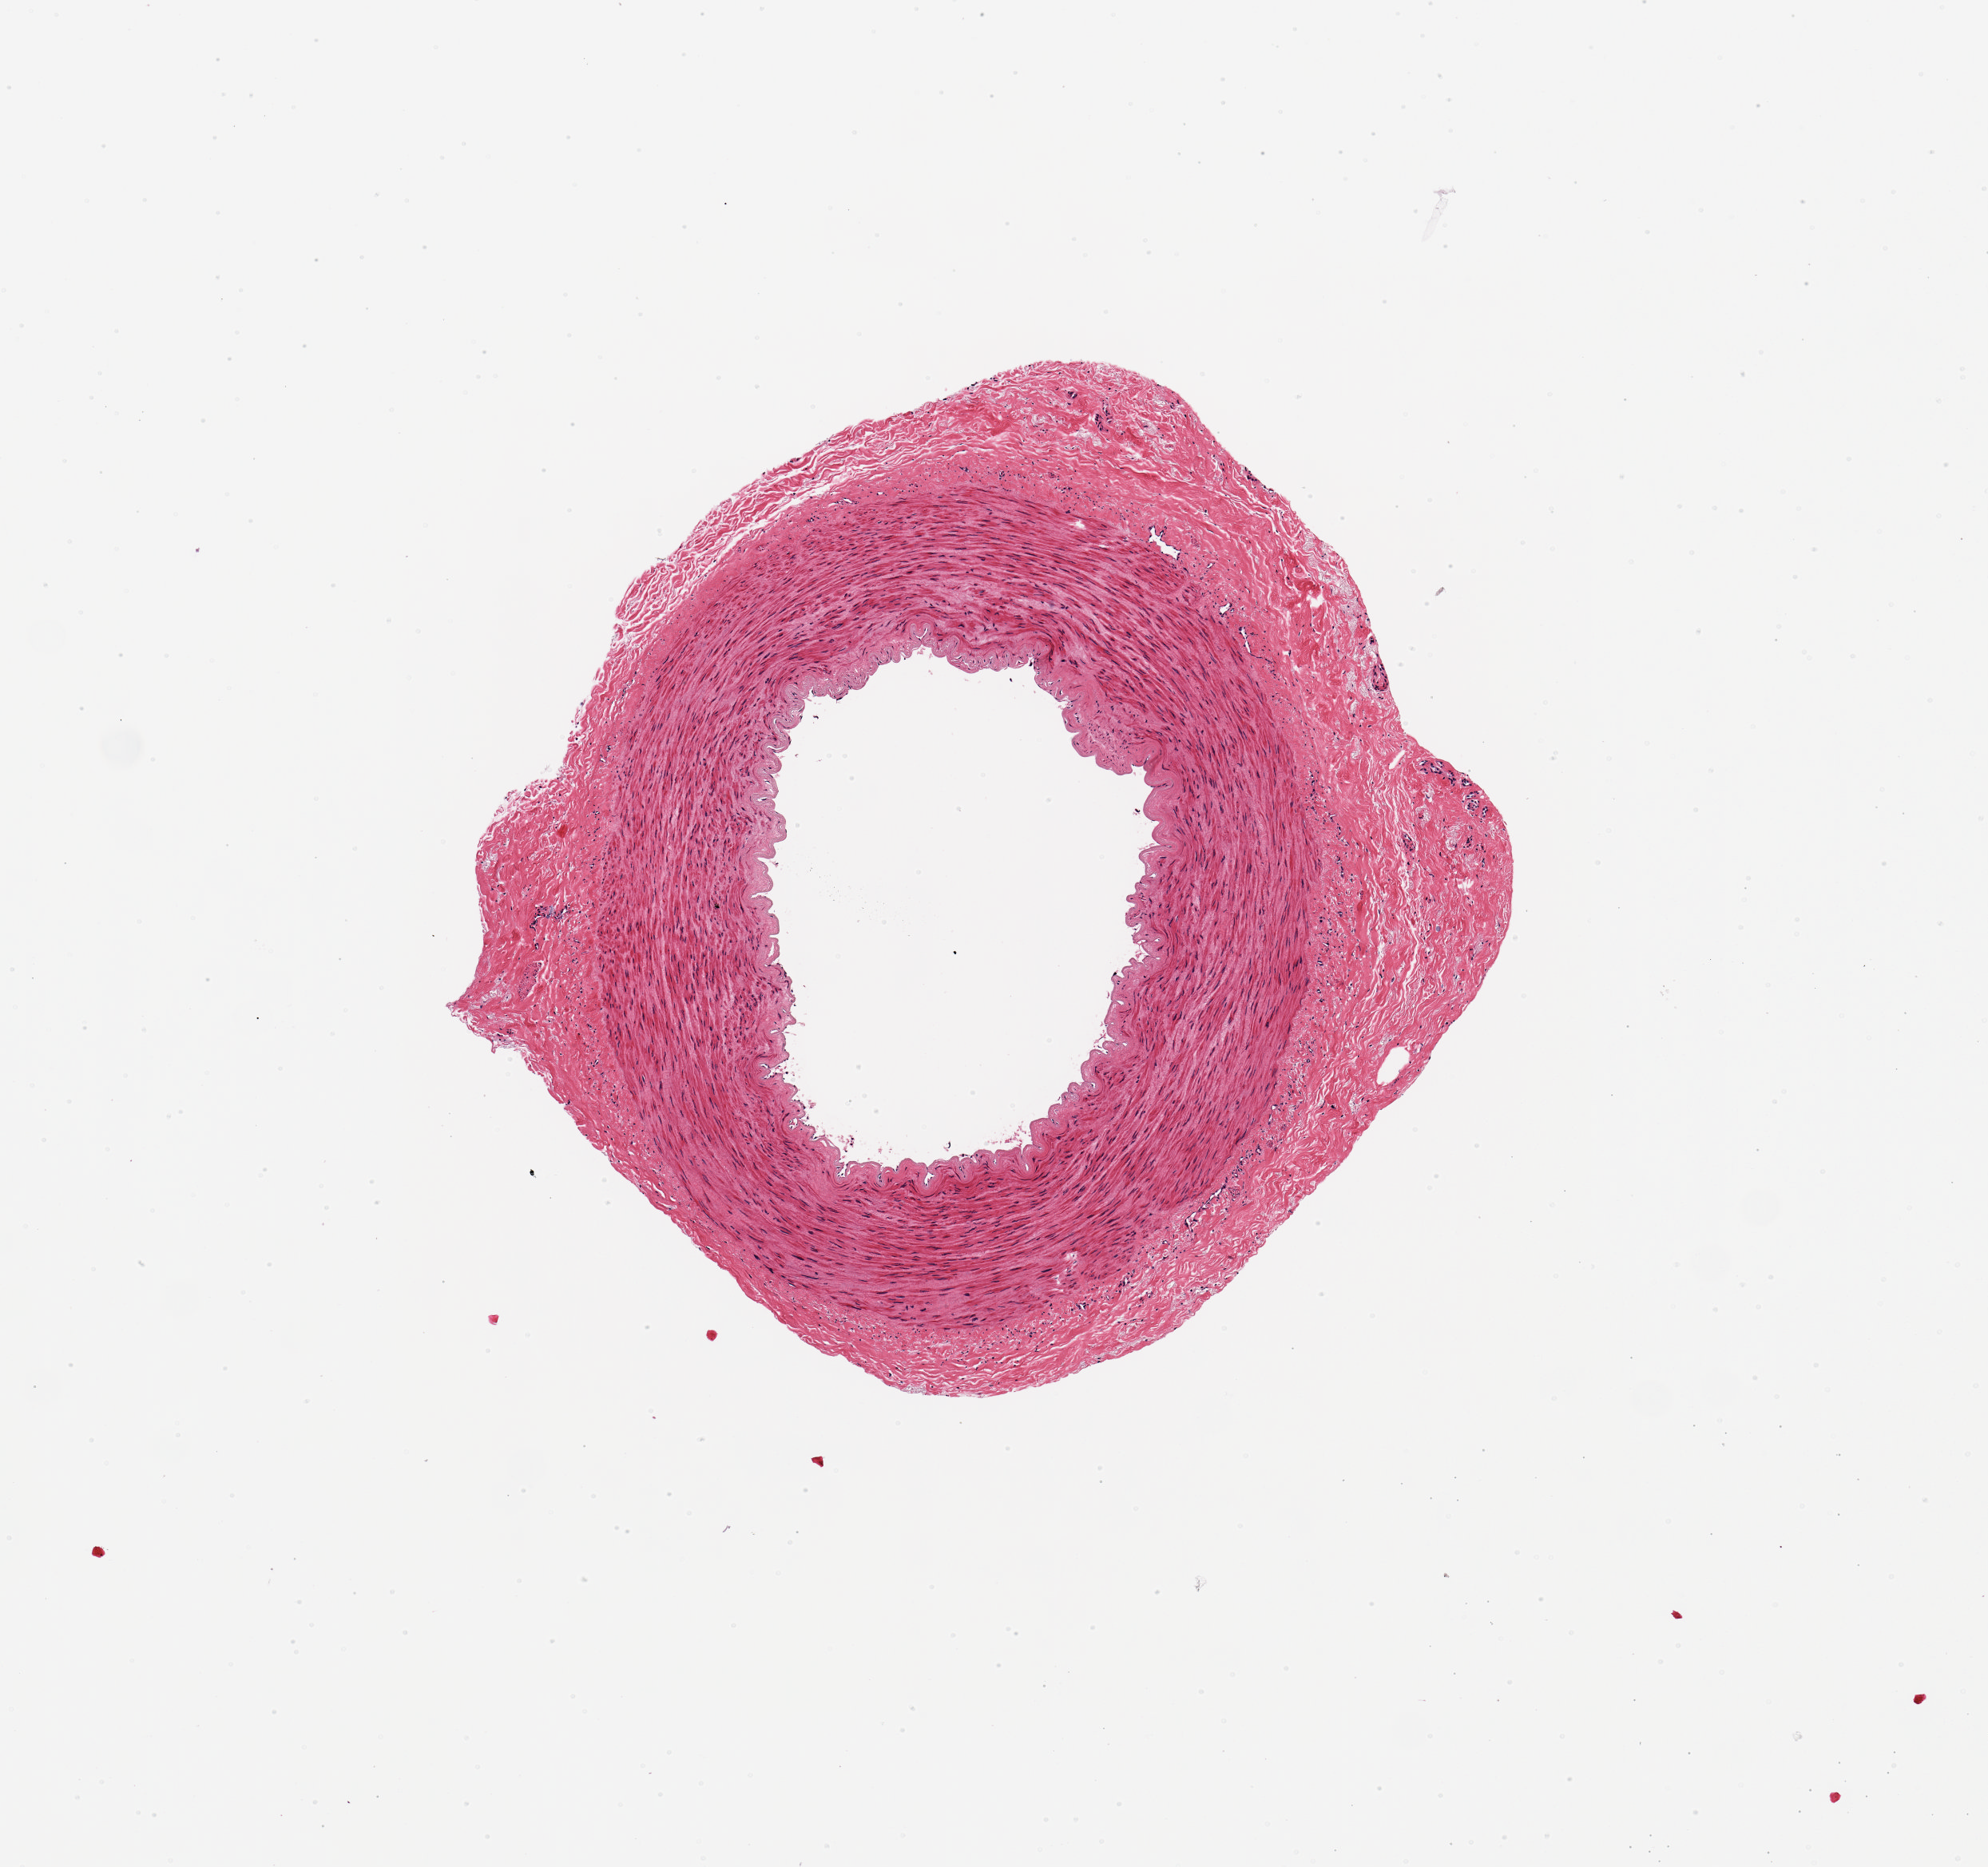
Digitized hematoxylin and eosin (H&E)-stained section, a low-resolution overview of the entire scanned area, about 4.9 x 4.6 mm; PAXgene-fixed paraffin-embedded (PFPE) section; target tissue: tibial artery; donor tissue sample. Donor sex: male.
Review note (as recorded): 2.6x2.5mm. Clean specimen.